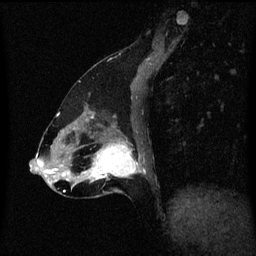
Breast MRI (dynamic contrast-enhanced), one sagittal slice. Position 25 of 60 along the scan axis. Dynamic contrast-enhanced series, image 2 of 3 at this slice position (ordered by acquisition). 1.5 T. TE 4.2 ms, TR 8.4 ms. 2 mm slice thickness. 256 × 256 image matrix, field of view 200 × 200 mm. Patient: female, 47 years.
Outlined on this slice (semi-automatically segmented with operator editing):
- analysis volume of interest (the breast-tissue region the enhancement analysis was run in; not a lesion): bounding box (x1, y1, x2, y2) in pixels: (85, 136, 143, 197)
- tumour enhancement mask (voxels above the 70 % enhancement threshold inside the analysis volume of interest): (85, 142, 140, 181)